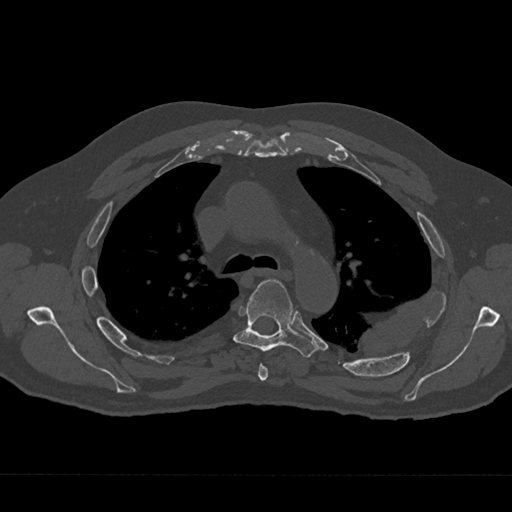
CT including the spine, one axial slice. Position 481 of 797 along the scan axis. 120 kVp. Bone window (W 1800 / L 400 HU). 0.5 mm slice thickness. 512 × 512 image matrix, field of view 377 × 377 mm. Male patient, age 75 years. Case-level facts recorded for this patient, not image findings: primary cancer: renal; vertebrae with lytic lesions (as recorded): T4.
Structures marked on this image (semi-automatic segmentation, software-assisted and operator-edited):
- T4 vertebra: bounding box <258,364,268,381> (left, top, right, bottom; pixels)
- T5 vertebra: <233,279,317,358>